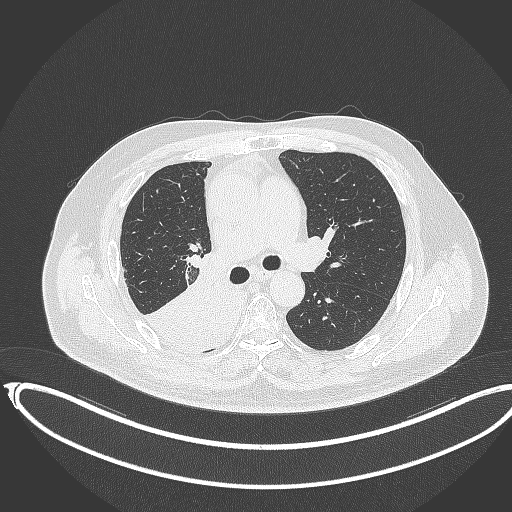
Chest CT, one axial slice. Position 219 of 403 along the scan axis. Reconstruction kernel B70f. 120 kVp. Lung window (W 1500 / L -600 HU). 512 × 512 image matrix, field of view 436 × 436 mm. Patient: male, 68 years. From the clinical record (not read from this slice): clinical TNM (as recorded): T2a N0 M0.
Outlined on this slice (rectangle marked by the reading radiologist):
- lung tumour (recorded histology: adenocarcinoma): box from (x=146, y=269) to (x=243, y=352) px